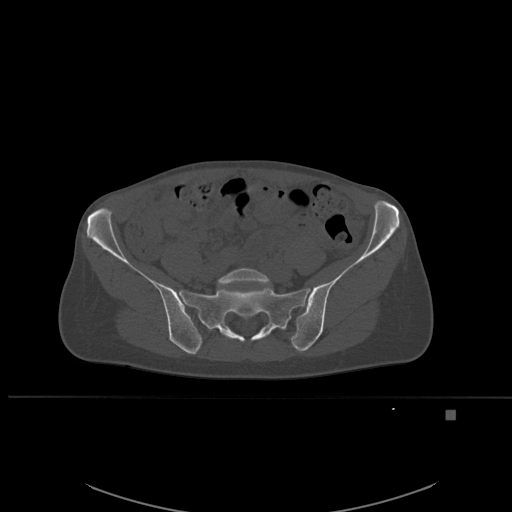
CT including the spine, one axial slice. Slice 158 of 537 in the series (ordered by position). Bone window (W 1800 / L 400 HU). 1.5 mm slice thickness. 512 × 512 image matrix. Female patient, age 45 years. Case-level facts recorded for this patient, not image findings: primary cancer: lung.
Outlined on this slice (semi-automatic segmentation, software-assisted and operator-edited):
- L5 vertebra: box from (x=217, y=268) to (x=271, y=288) px